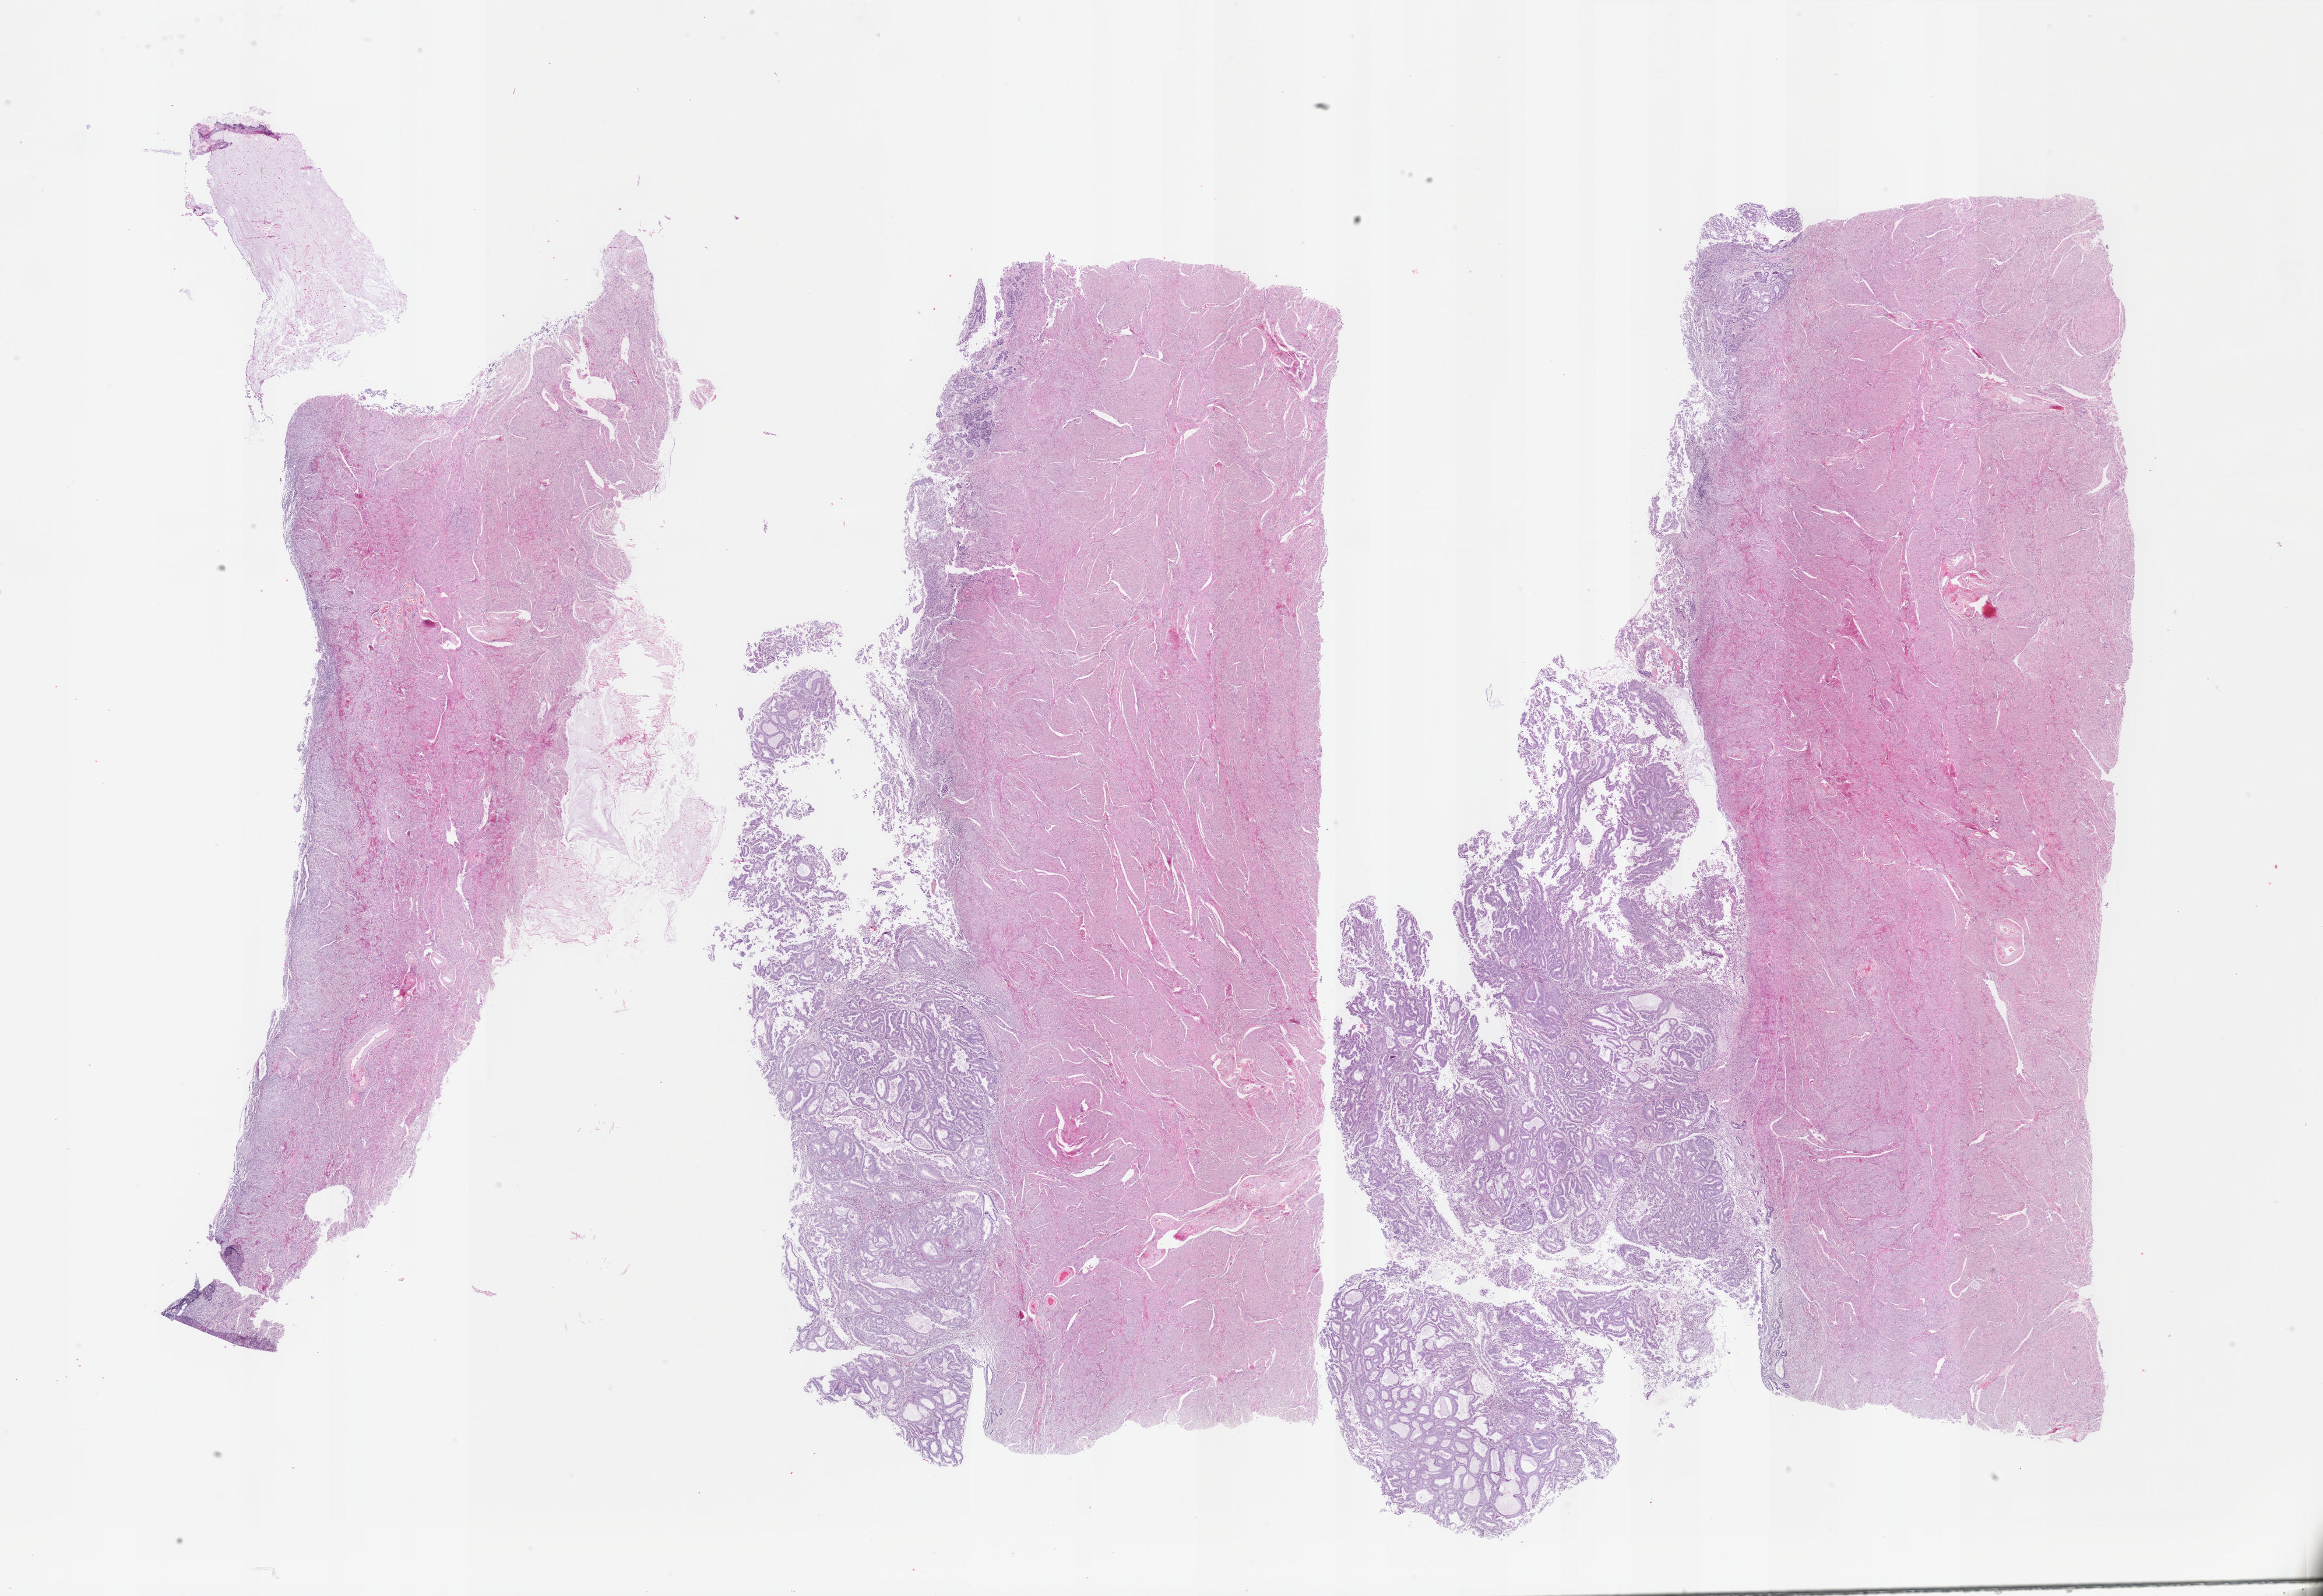
H&E whole-slide image — low-resolution overview of the scanned area, about 31.6 x 21.7 mm, formalin-fixed paraffin-embedded (FFPE) diagnostic section, sample: primary tumour, uterus. Female patient; age at initial diagnosis 58 years. Histologic grade: G1 (well differentiated).
• histologic diagnosis: Endometrioid adenocarcinoma, NOS
• FIGO stage: IA